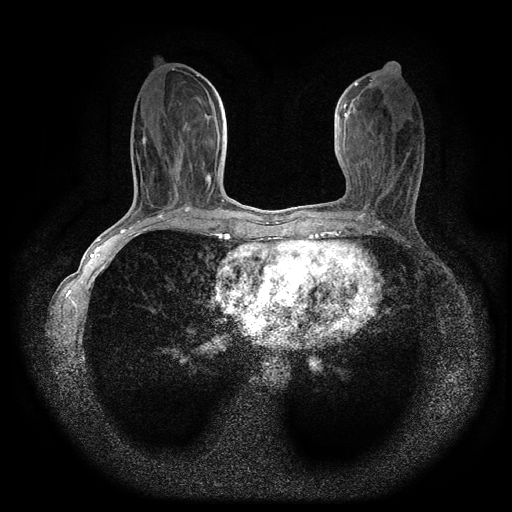
Breast MRI (dynamic contrast-enhanced, multi-phase), one axial slice; position 38 of 116 along the scan axis; dynamic contrast-enhanced series, time point 2 of 5 at this slice position (early post-contrast); 1.5 T; TE 2.7 ms, TR 5.4 ms; 2 mm slice thickness; 512 × 512 image matrix, field of view 330 × 330 mm. Female patient, age 49 years.
Outlined on this slice (semi-automatically segmented with operator editing):
- breast lesion (labelled benign in the annotation): bounding box <203,171,213,188> (left, top, right, bottom; pixels)